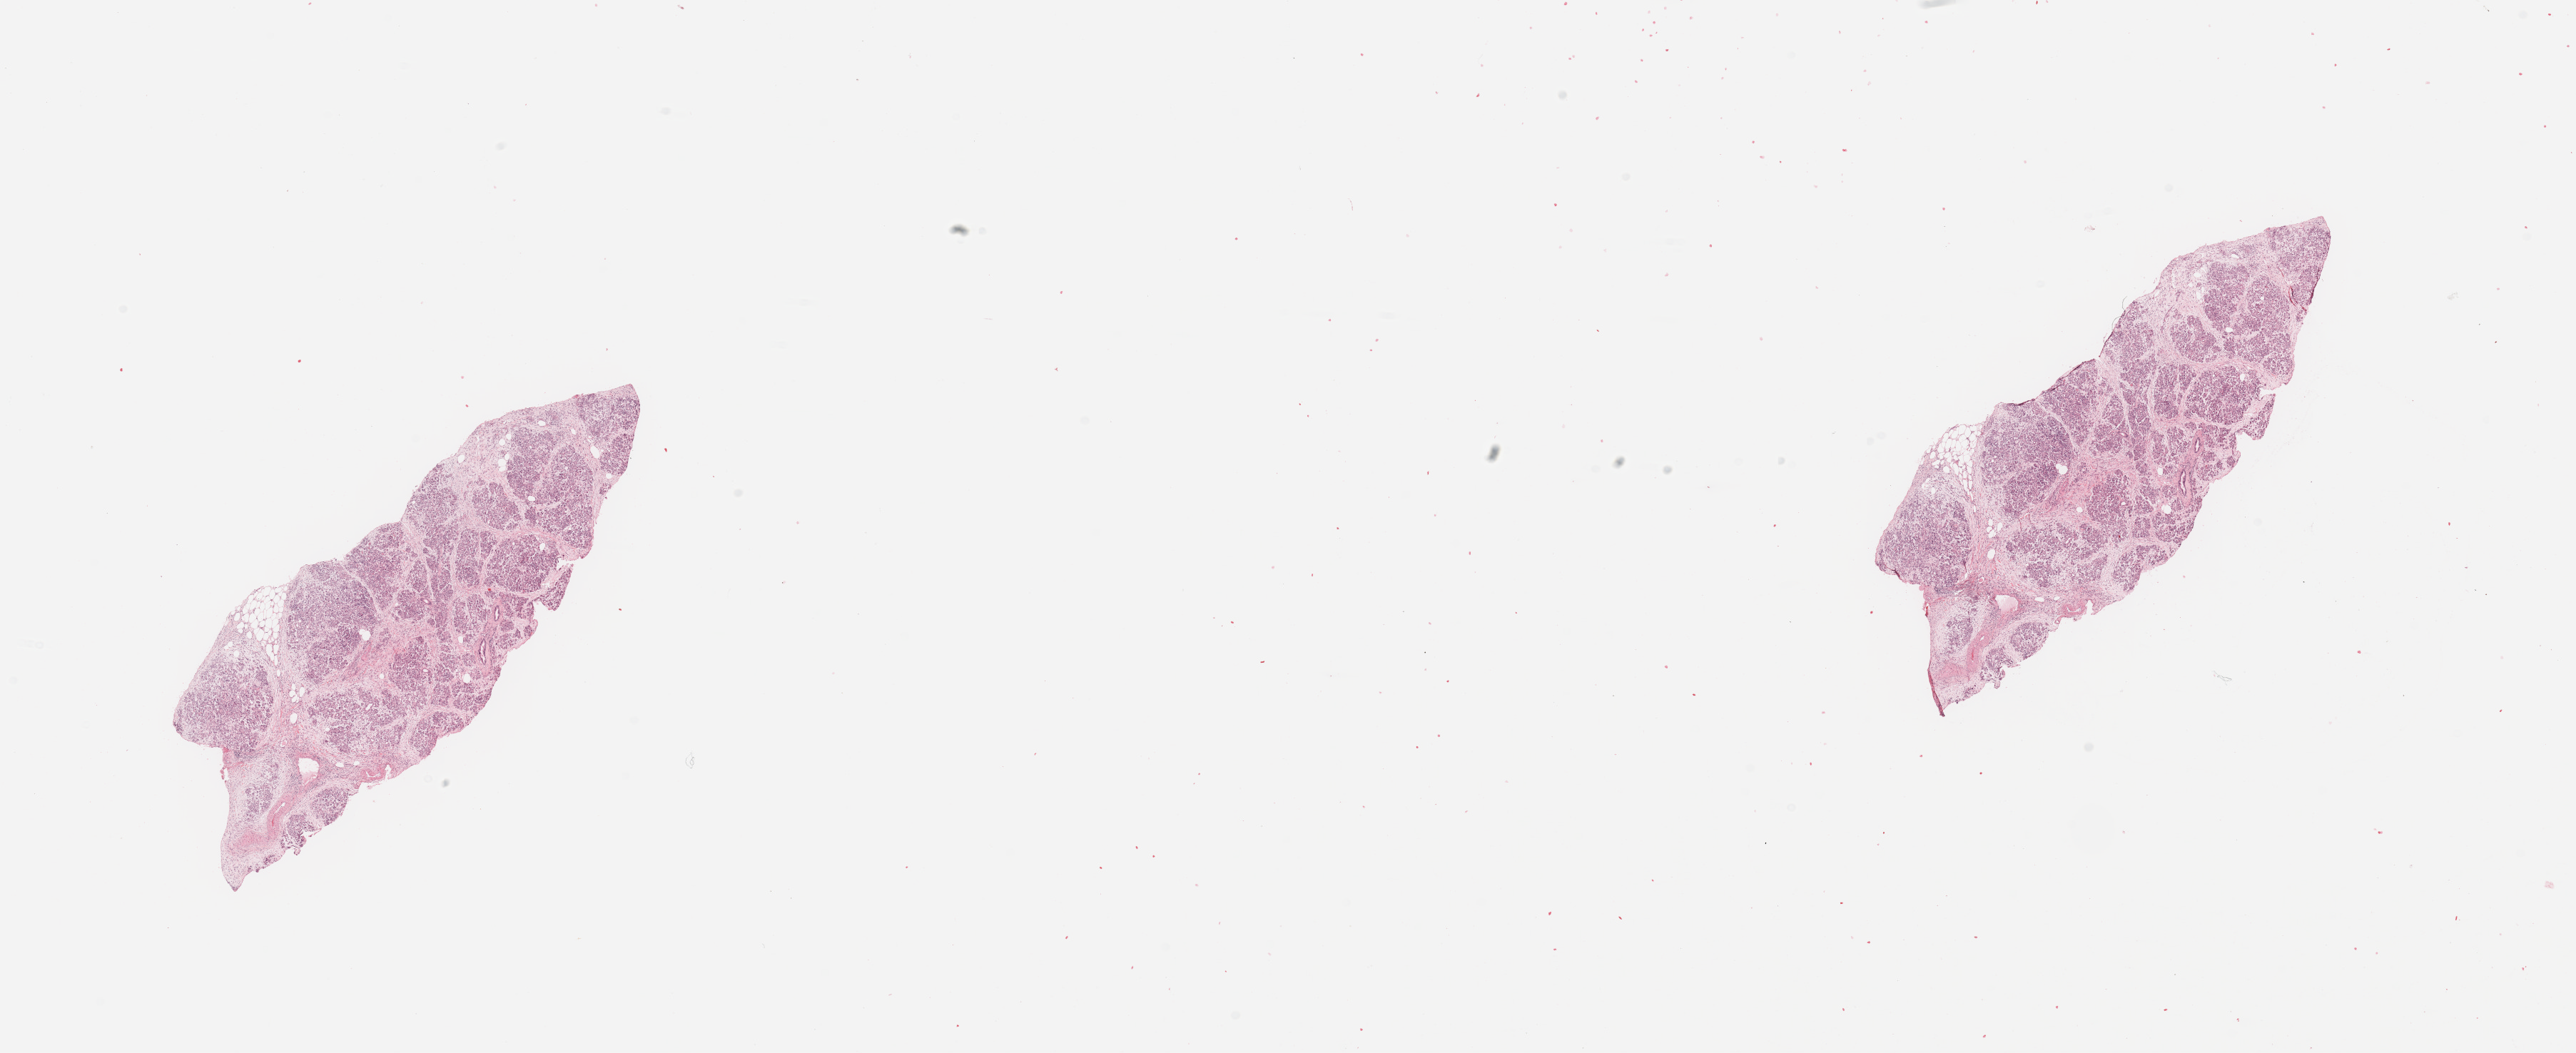
Digitized H&E tissue section (whole slide), low-resolution overview of the scanned area, about 28.5 x 11.7 mm; normal (non-tumour) tissue sample, sampled site: pancreas. 62-year-old female patient.
* this section: normal (non-tumour) tissue from the same patient
* patient diagnosis: Infiltrating duct carcinoma, NOS